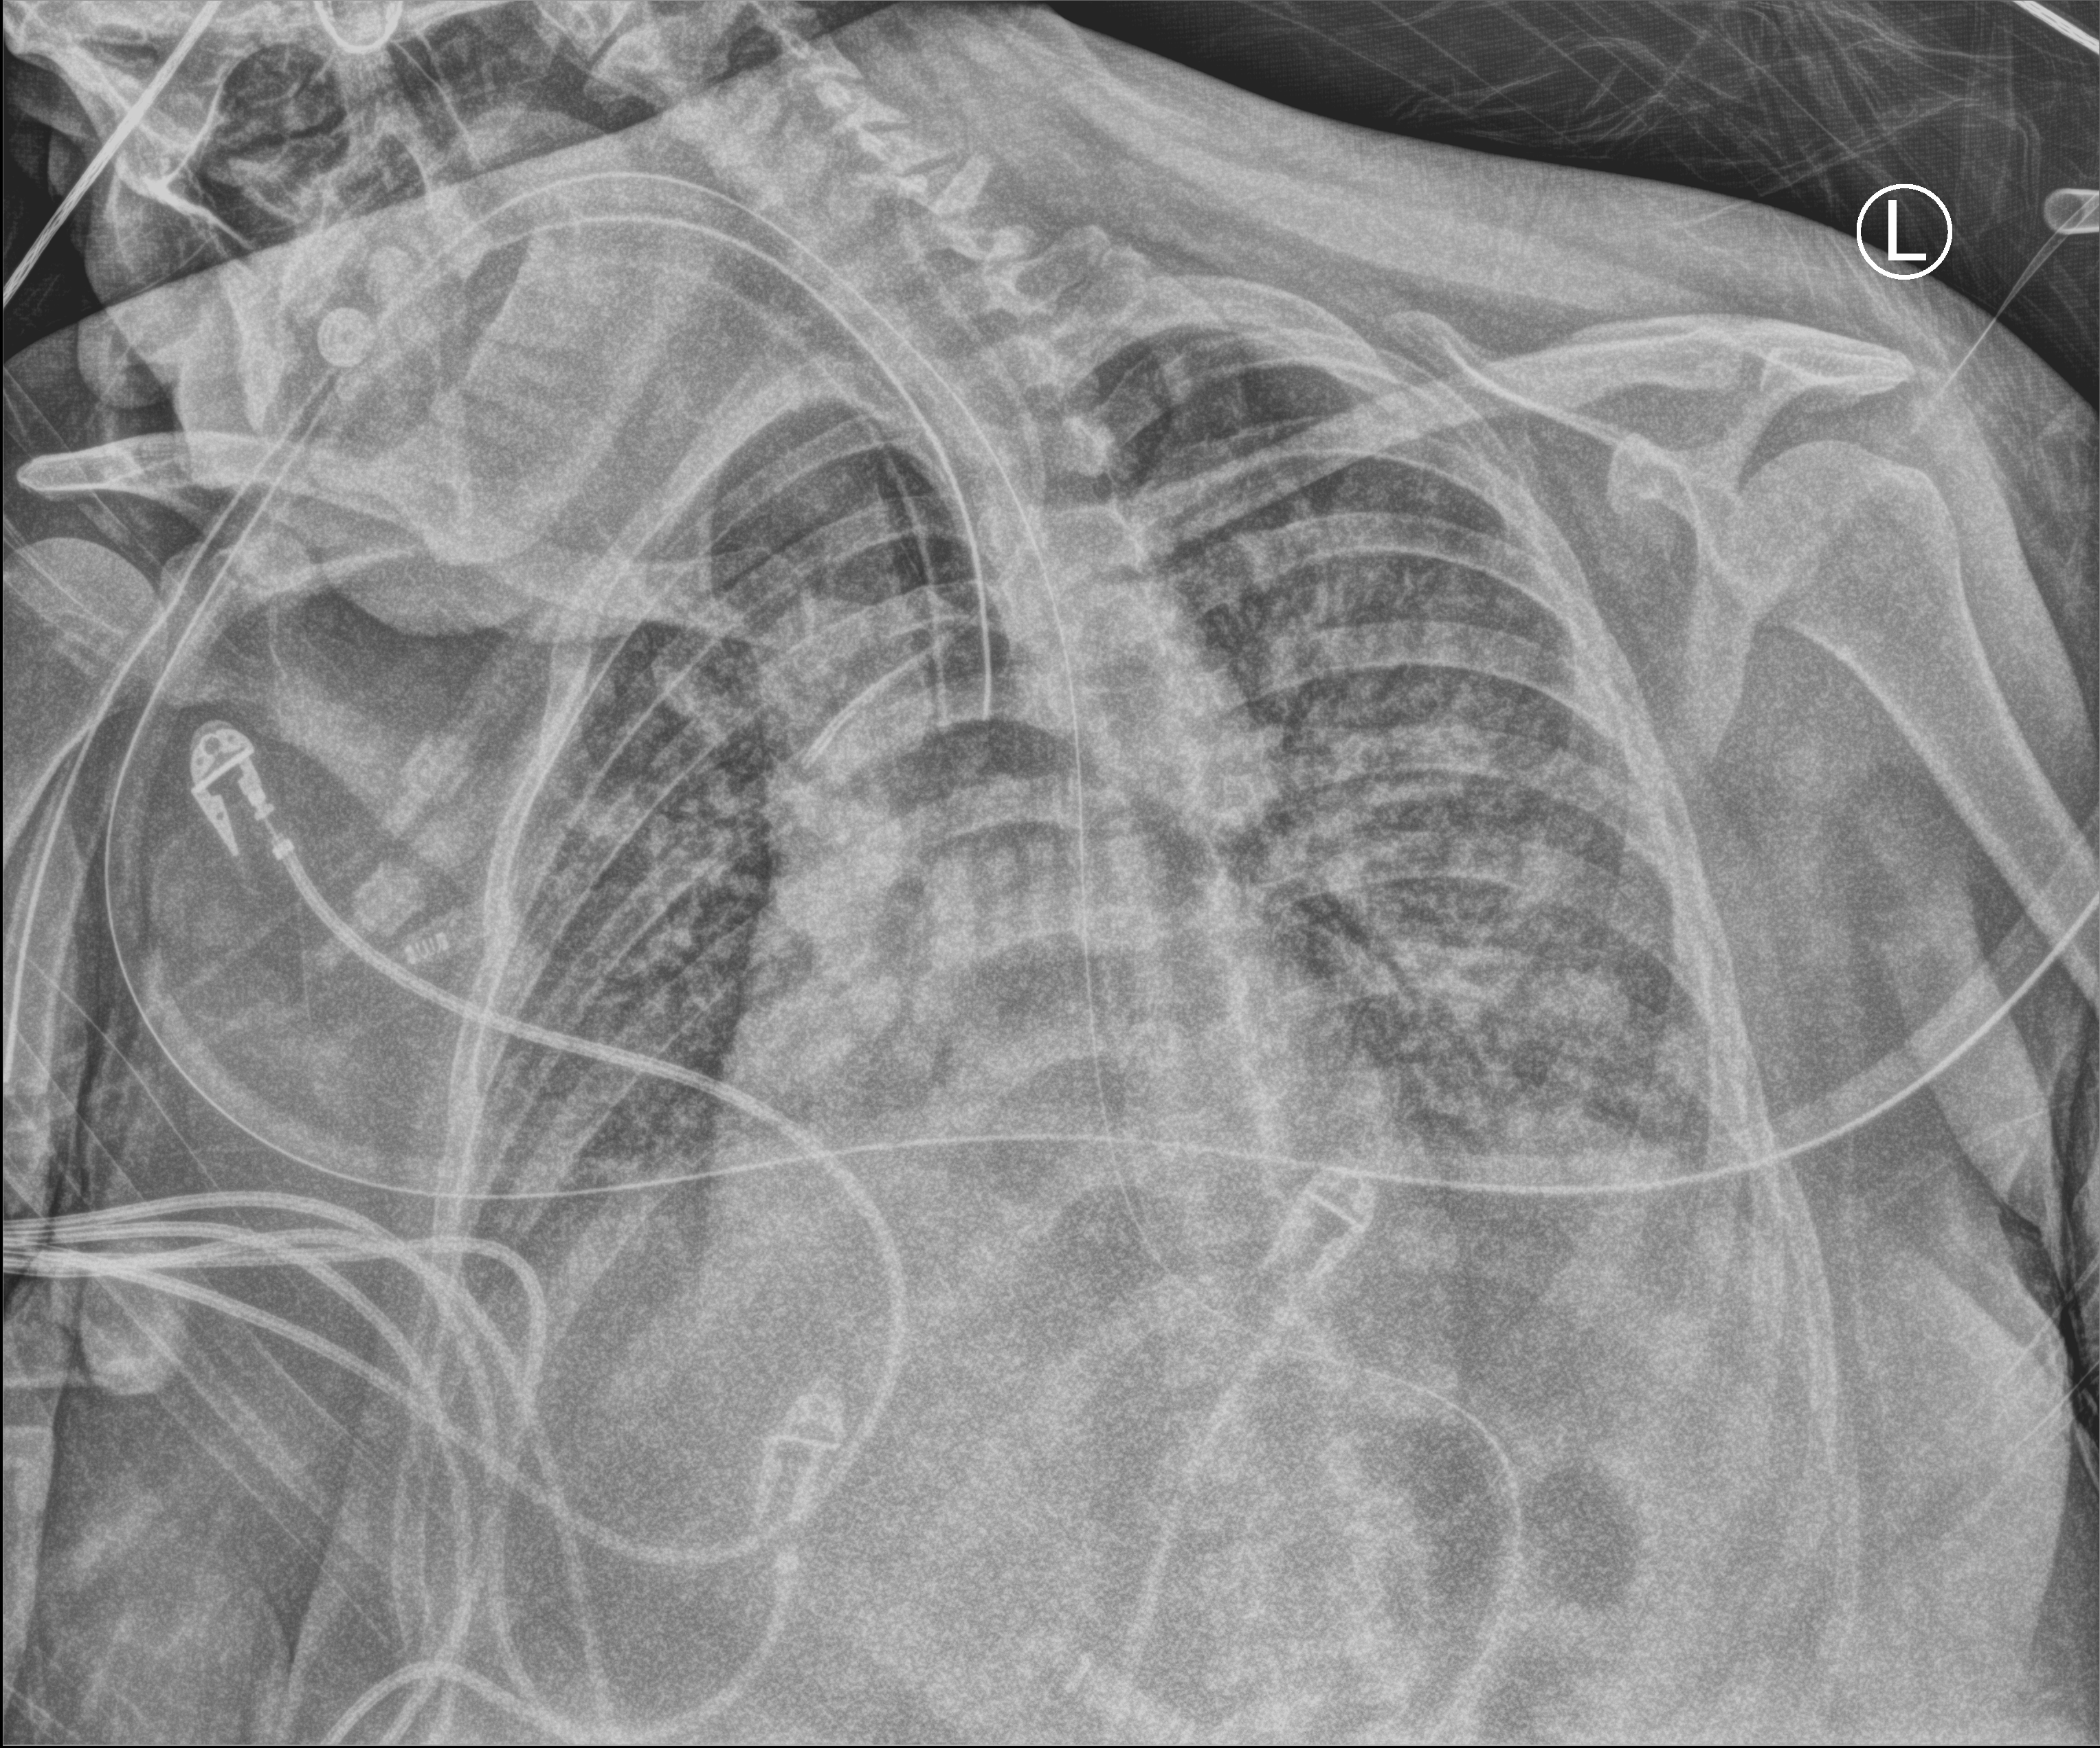
Chest X-ray (portable), anteroposterior (AP) projection. Patient hospitalised with COVID-19; female, aged 18–59 years.
Hospital-stay facts (about this admission, not read from this image; timing relative to this image not recorded): admitted to intensive care during this hospital stay: no; mechanically ventilated during this hospital stay: yes.